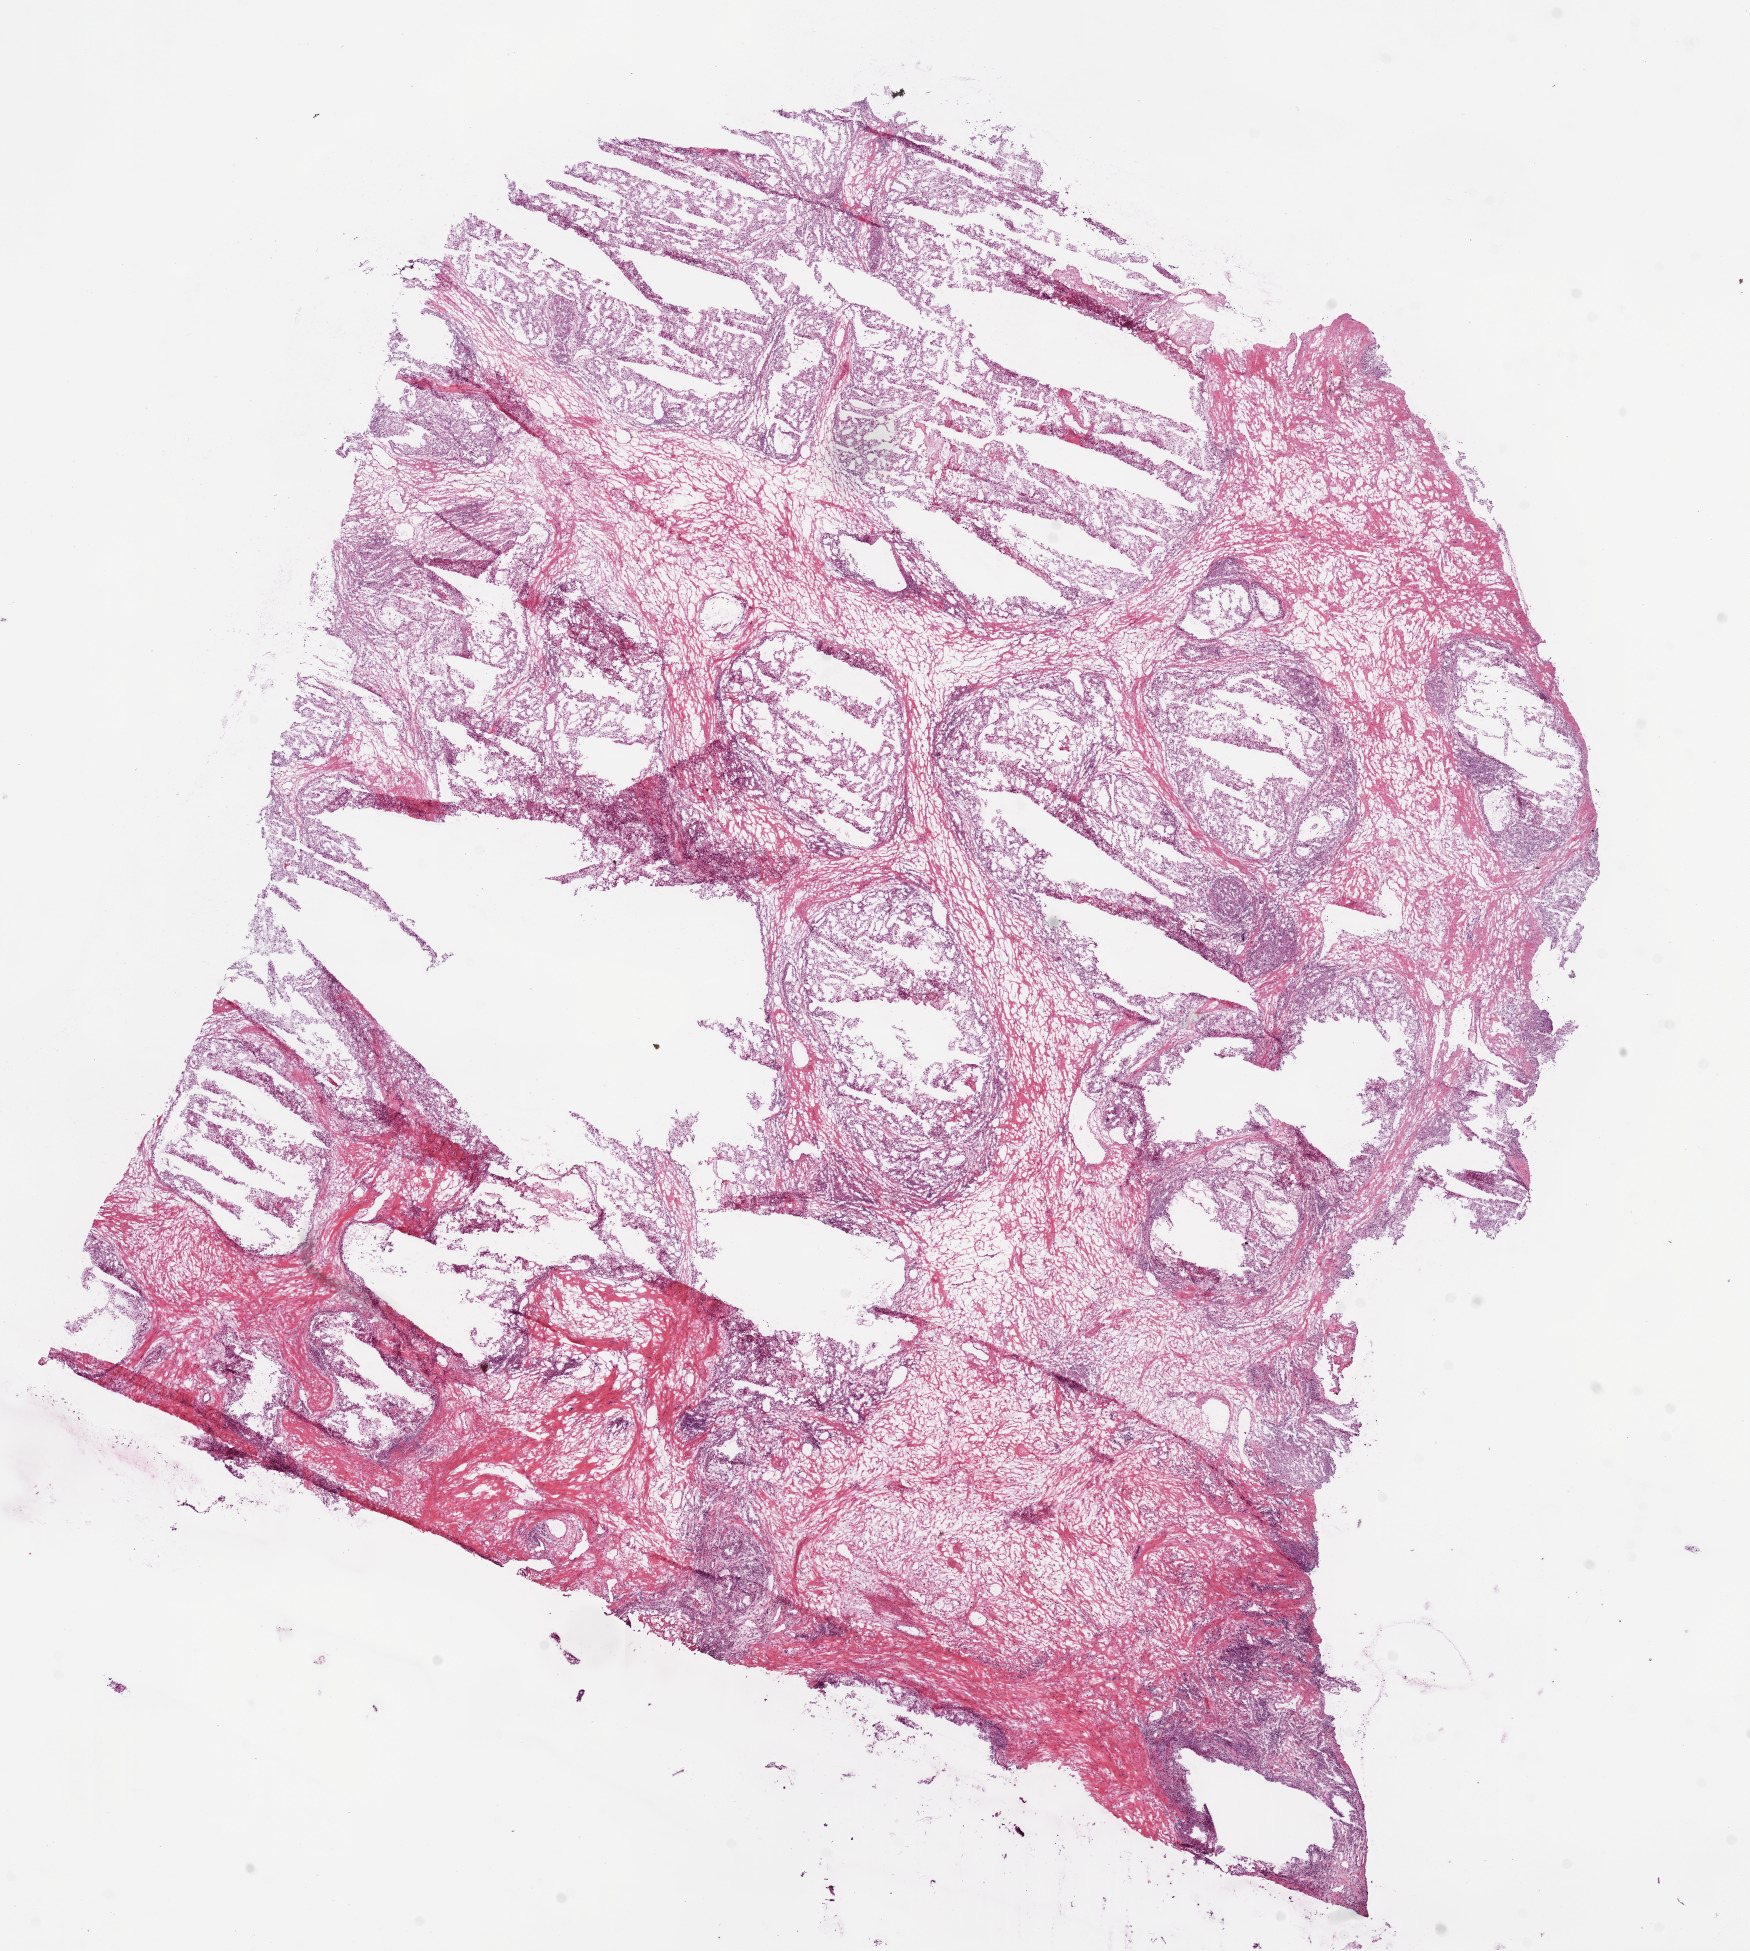
Digitized Hematoxylin and eosin (H&E) stained tissue section (whole slide) — shown as a low-resolution overview of the whole scanned area (about 14.0 x 15.7 mm, slide scanned at 20x); frozen section from the bottom of the tissue portion; sample: primary tumour, kidney. Male, age 40 years at initial diagnosis. Histologic grade: G3 (poorly differentiated). Pathologist review of this section (percent, as recorded): tumour cells 70%, tumour nuclei 75%, normal cells 0%, stromal cells 30%, necrosis 0%.
* diagnosis: Clear cell adenocarcinoma, NOS
* lymph nodes positive (case pathology): 0 of 5 examined
* AJCC pathologic stage: III